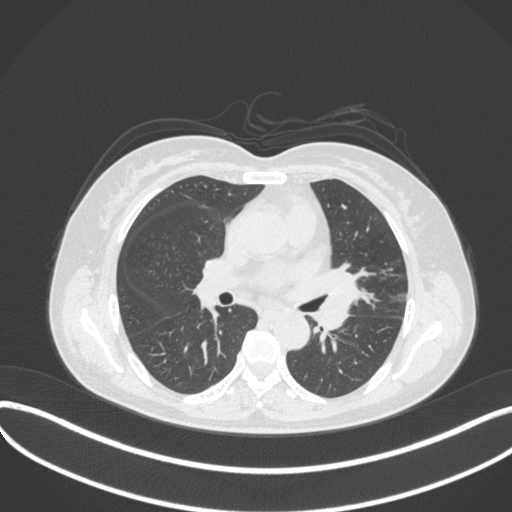
Chest CT, one axial slice; slice 193 of 373 in the series (ordered by position); lung window (W 1500 / L -600 HU); 1 mm slice thickness; 512 × 512 image matrix. Female patient, age 54 years. From the clinical record (not read from this slice): clinical TNM (as recorded): T2a N1 M0.
Structures marked on this image (bounding box drawn by a radiologist):
- lung tumour (recorded histology: small cell carcinoma): bounding box (x1, y1, x2, y2) in pixels: (310, 263, 361, 336)